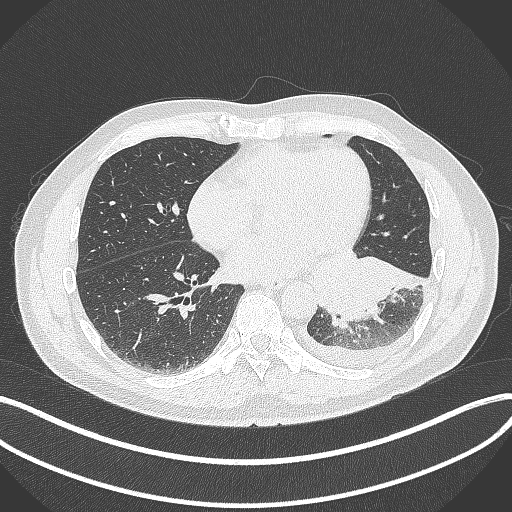
Chest CT, one axial slice; reconstruction kernel B70f; 120 kVp; lung window (W 1500 / L -600 HU); 512 × 512 image matrix, field of view 400 × 400 mm. Patient: male, 58 years. Case-level facts recorded for this patient, not image findings: clinical TNM (as recorded): T3 N1 M1b.
Annotated regions visible in this slice (bounding box drawn by a radiologist):
- lung tumour (recorded histology: small cell carcinoma): bounding box (x1, y1, x2, y2) in pixels: (305, 248, 418, 323)